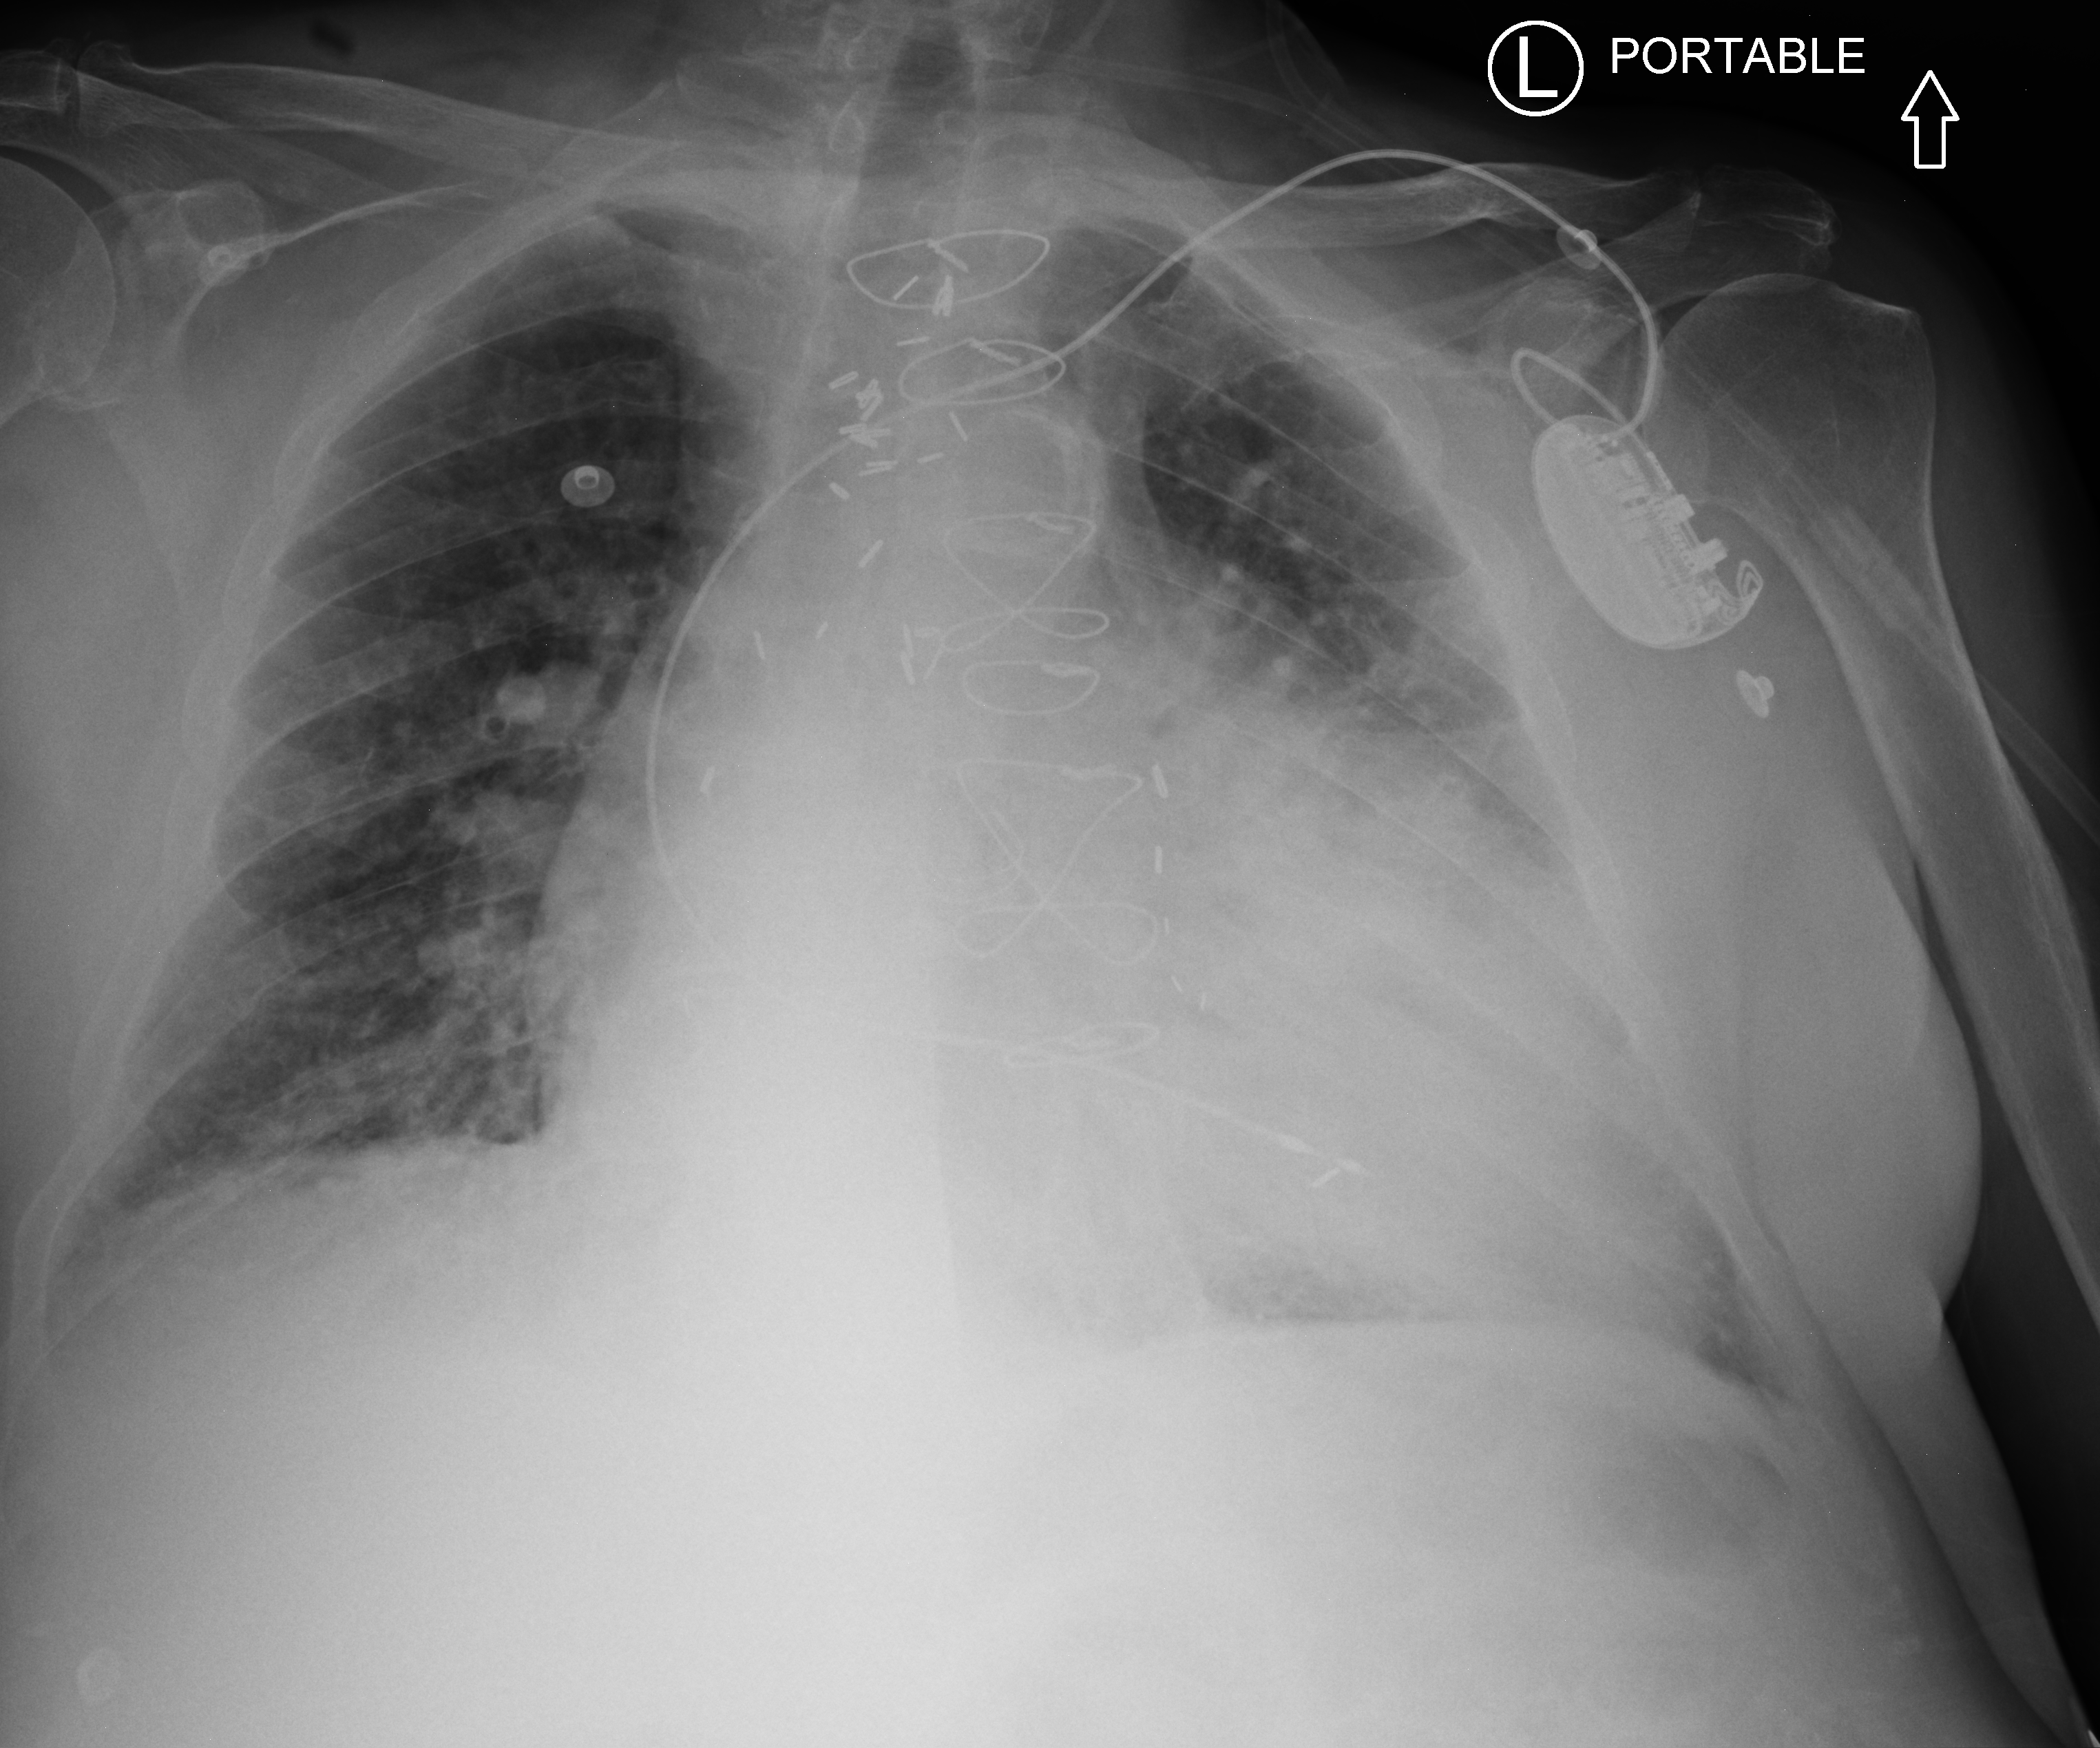
Portable chest radiograph, anteroposterior (AP) projection. Male patient hospitalised with COVID-19, age 75–90 years.
From the hospital-stay record, not from the radiograph (when in the stay this image was taken is not recorded): admitted to intensive care during this hospital stay: yes.